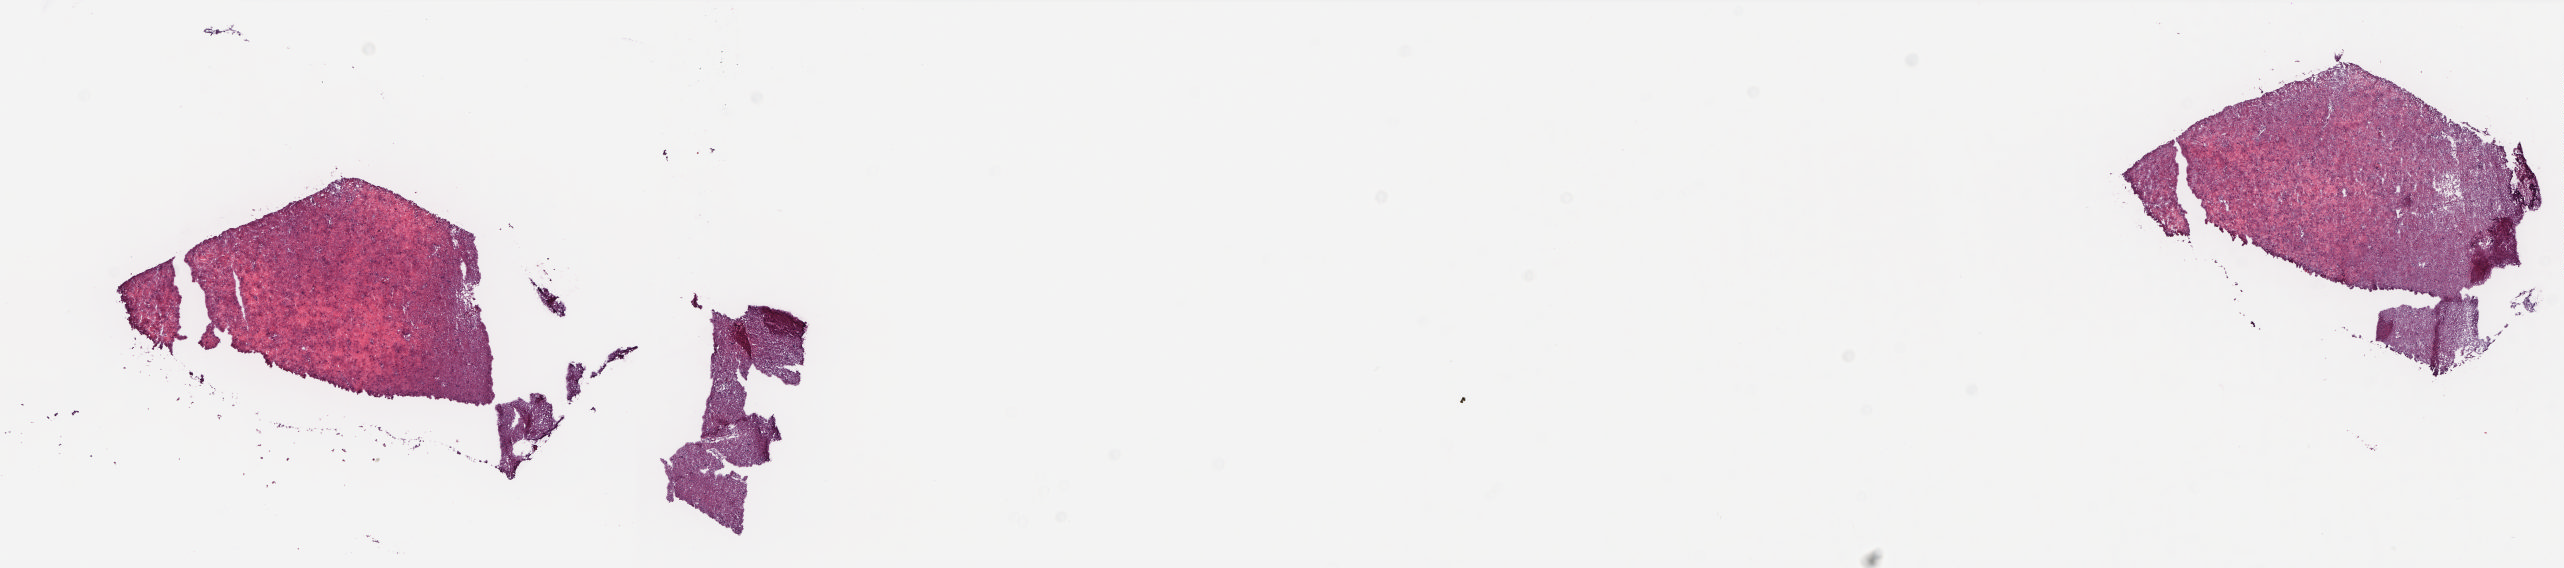
Whole-slide histology image, H&E-stained, low-resolution overview of the scanned area, about 20.7 x 4.6 mm (slide scanned at 20x); frozen section; sample: solid tissue normal (non-tumour tissue), brain. Composition of this section per pathologist review: tumour cells 0%, tumour nuclei 0%, normal cells 30%, stromal cells 70%, necrosis 0%. Infiltration values recorded for this section: lymphocyte infiltration 0%, monocyte infiltration 0%, neutrophil infiltration 0%.
This section: solid tissue normal sample (biorepository sample class).